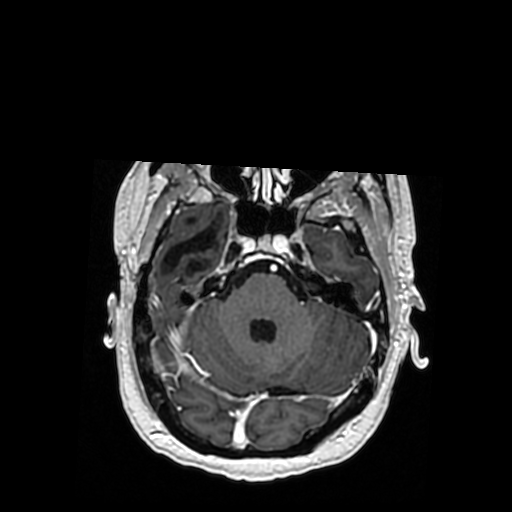
Brain MRI from a brain-tumour surgery series, one axial slice. Position 248 of 364 along the scan axis. T1-weighted post-contrast. 0.5 mm slice thickness. 512 × 512 image matrix. From the clinical record (not read from this slice): histopathology: Oligodendroglioma; WHO grade: 3; IDH mutation: yes; tumour location: Right Posterior Temporal Inferior Parietal.
Outlined on this slice (manually delineated by an expert):
- previous resection cavity: box from (x=163, y=219) to (x=218, y=276) px